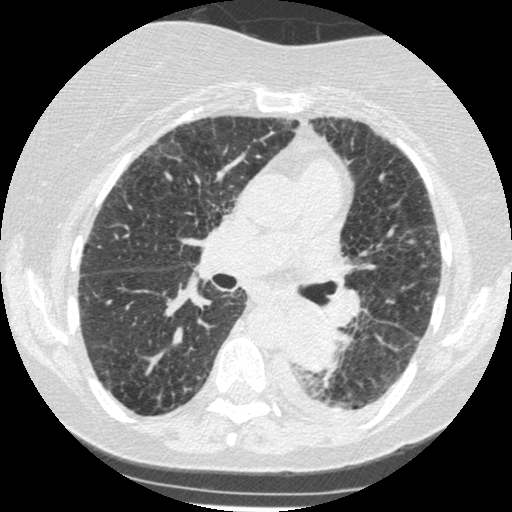
Low-dose screening chest CT, one axial slice. Slice 143 of 341 in the series (ordered by position). Reconstruction kernel STANDARD. Lung window (W 1500 / L -600 HU). 1.25 mm slice thickness. 512 × 512 image matrix, field of view 310 × 310 mm.
Structures marked on this image (manually delineated by an expert):
- lesion 1 (tumor, lower lobe of left lung): box from (x=285, y=307) to (x=337, y=372) px